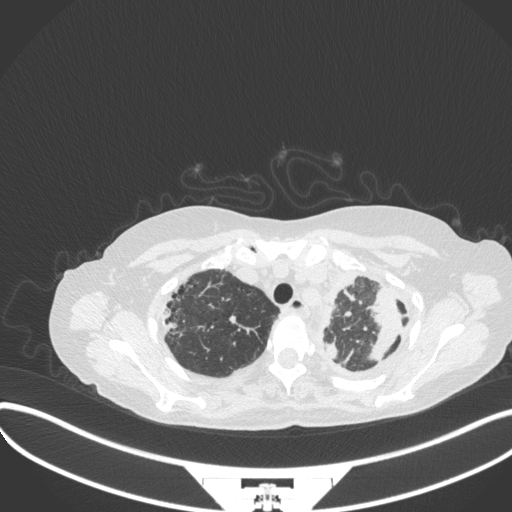
Chest CT, one axial slice. Position 283 of 373 along the scan axis. 120 kVp. Lung window (W 1500 / L -600 HU). 1 mm slice thickness. 512 × 512 image matrix, field of view 400 × 400 mm. Patient: female, 56 years. Case-level facts recorded for this patient, not image findings: clinical TNM (as recorded): T1 N0 M0.
Outlined on this slice (rectangle marked by the reading radiologist):
- lung tumour (recorded histology: adenocarcinoma): bounding box [x1, y1, x2, y2] px = [358, 282, 406, 363]